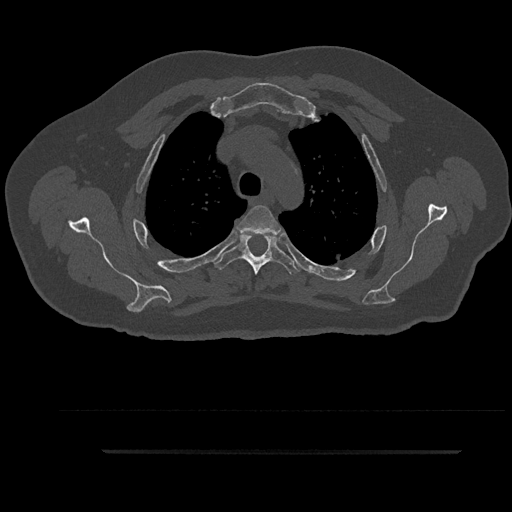
CT including the spine, one axial slice. Slice 689 of 797 in the series (ordered by position). Reconstruction kernel Br40s/3. Bone window (W 1800 / L 400 HU). 0.5 mm slice thickness. 512 × 512 image matrix, field of view 432 × 432 mm. Patient: male, 63 years. Case-level facts recorded for this patient, not image findings: primary cancer: renal.
Outlined on this slice (semi-automatically segmented with operator editing):
- T3 vertebra: bounding box (x1, y1, x2, y2) in pixels: (237, 205, 281, 236)
- T4 vertebra: (213, 234, 300, 275)